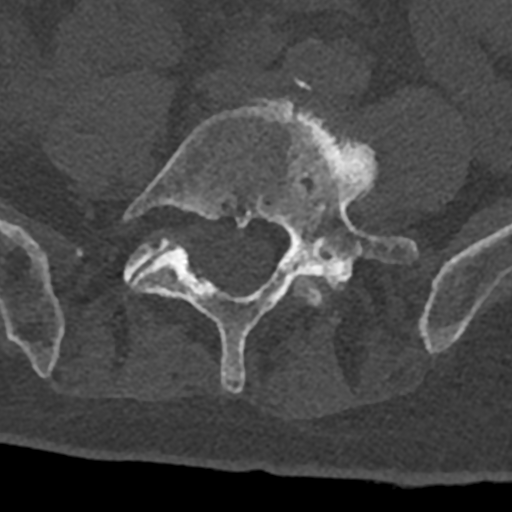
CT including the spine, one axial slice; position 204 of 797 along the scan axis; bone window (W 1800 / L 400 HU); 0.5 mm slice thickness; 512 × 512 image matrix. Male patient, age 74 years. Case-level facts recorded for this patient, not image findings: primary cancer: renal.
Outlined on this slice (semi-automatic segmentation, software-assisted and operator-edited):
- L4 vertebra: bounding box <288,275,324,306> (left, top, right, bottom; pixels)
- L5 vertebra: <123,99,418,393>